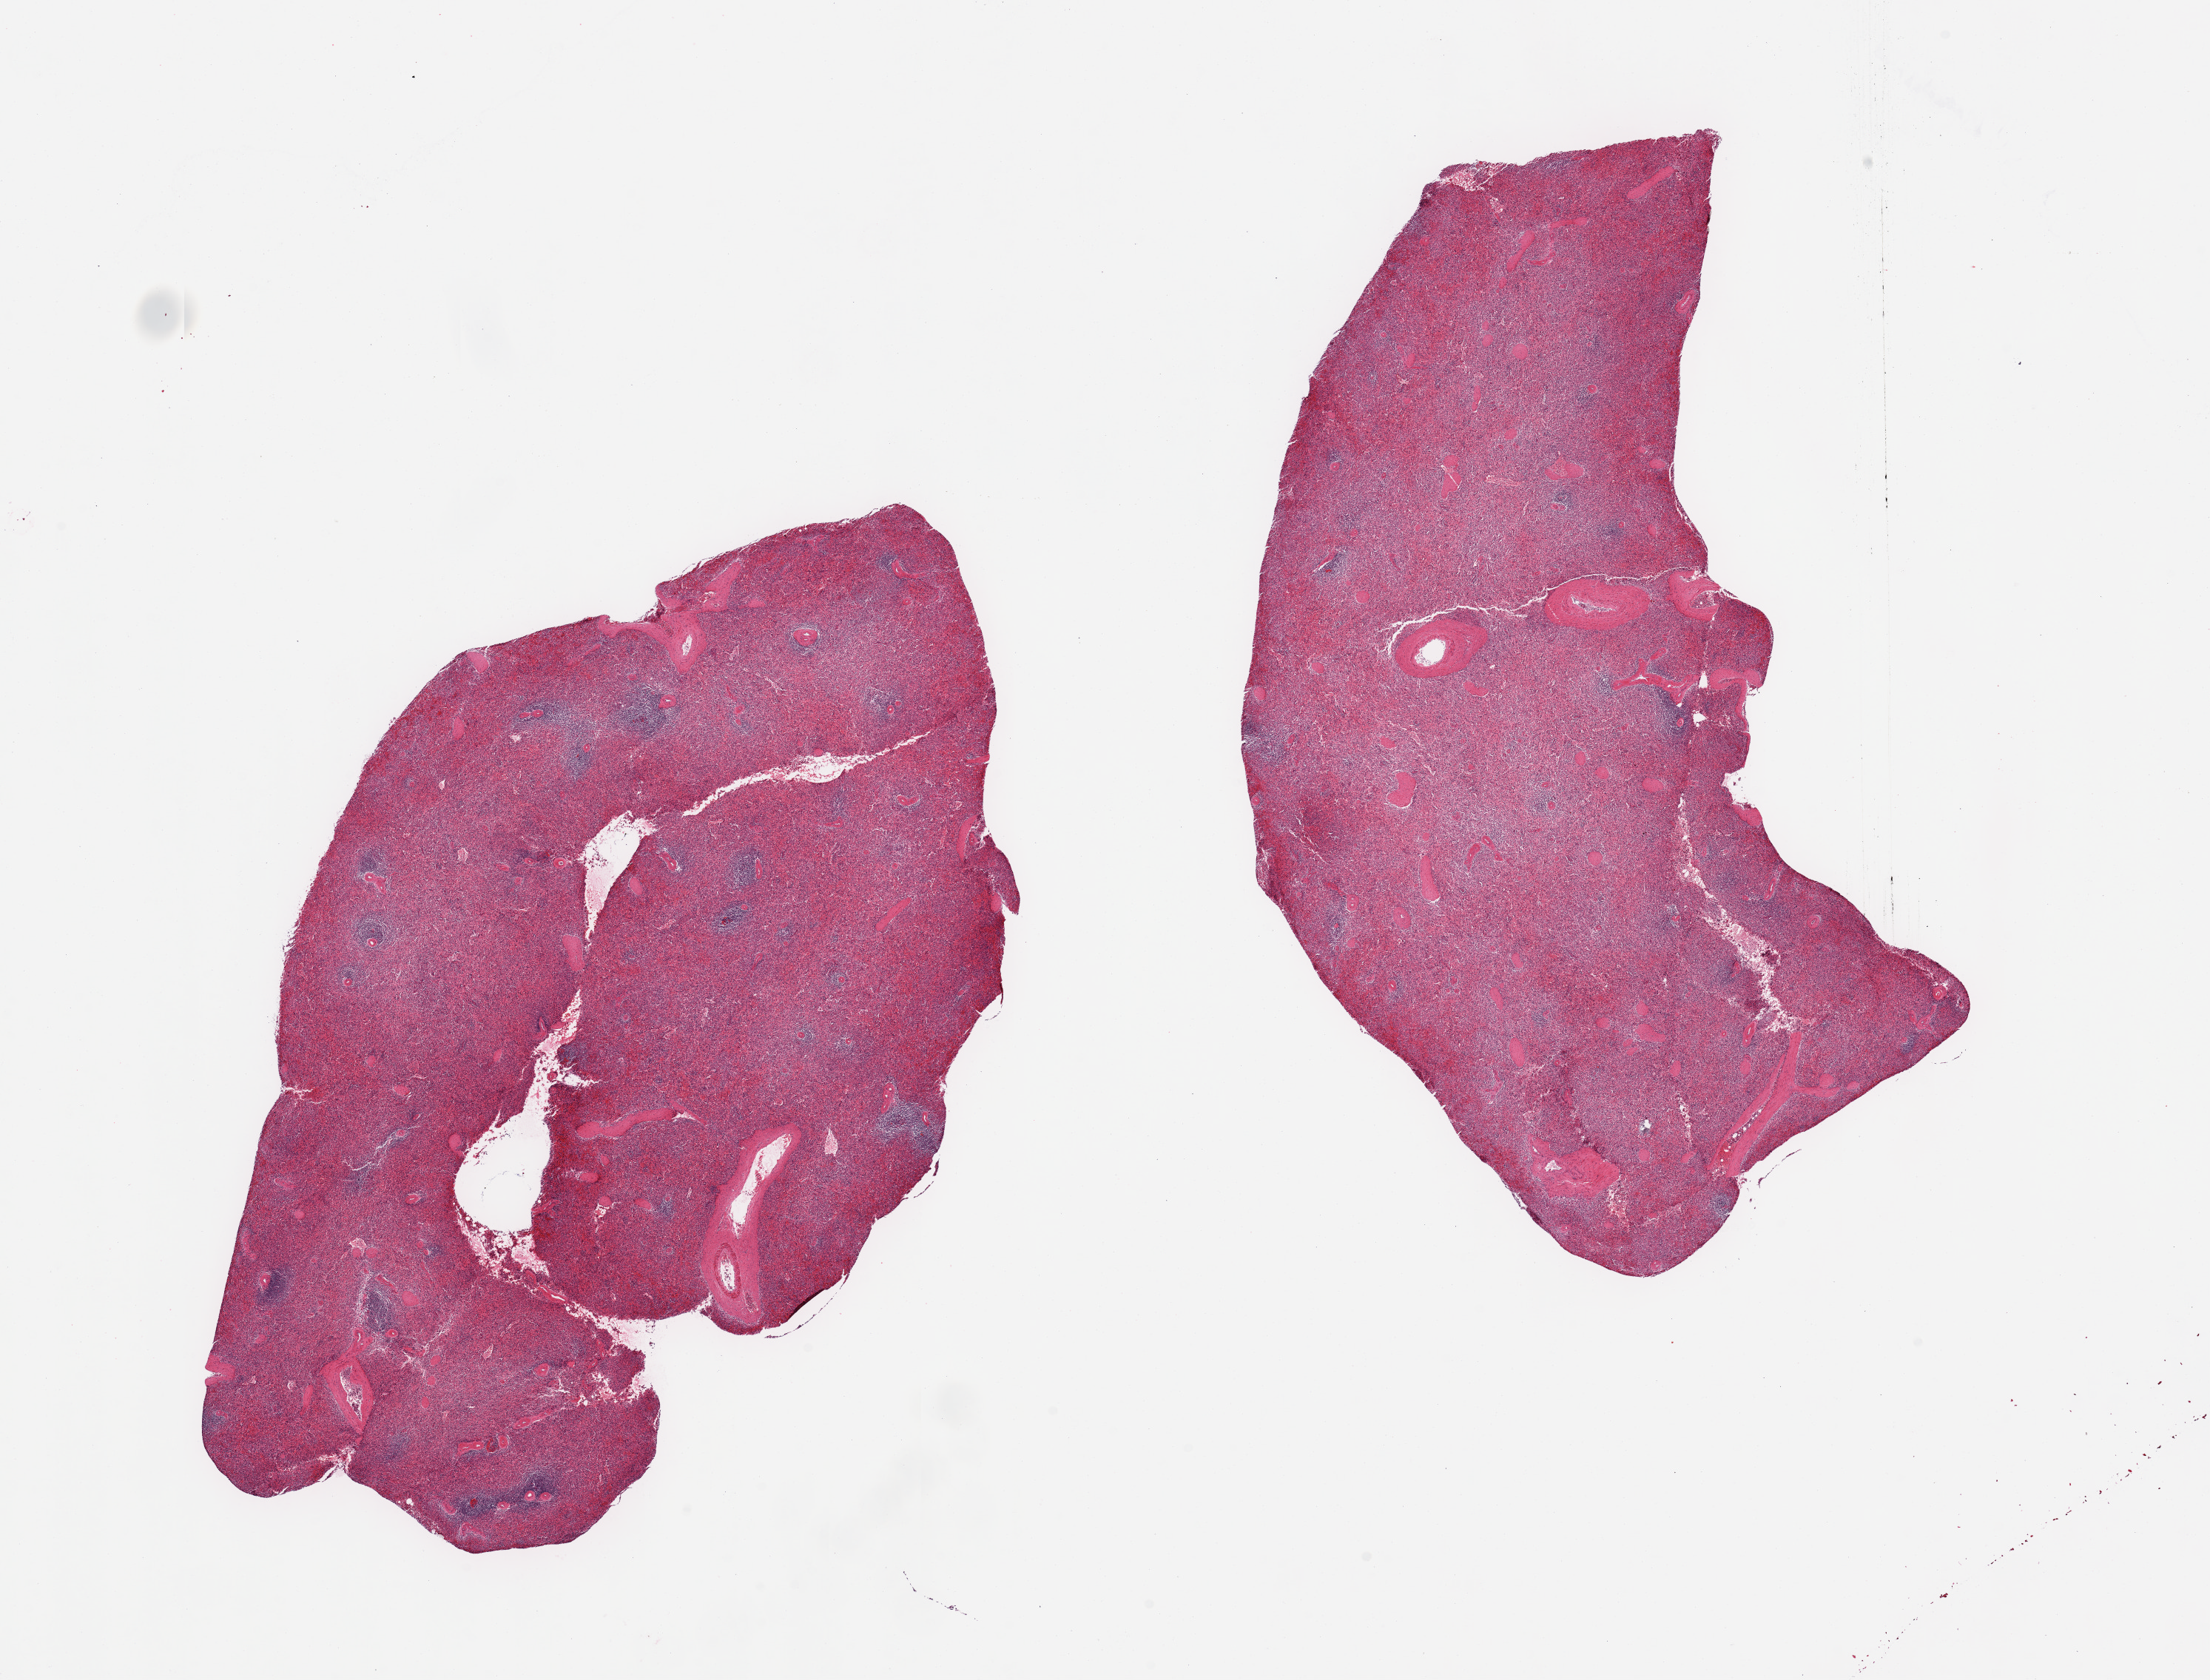
Hematoxylin and eosin (H&E) whole-slide image, brightfield, shown as a low-resolution overview of the whole scanned area (about 23.6 x 18.0 mm), PAXgene-fixed, paraffin-embedded tissue, target tissue: spleen, donor tissue sample. Donor: female.
Reviewer comment on this tissue sample: 2 pieces, no abnormalities.